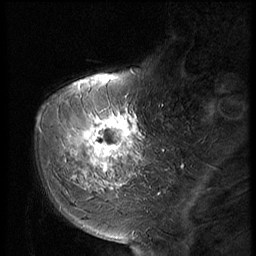
Breast MRI (dynamic contrast-enhanced), one sagittal slice. Position 16 of 56 along the scan axis. Dynamic contrast-enhanced series, image 2 of 2 at this slice position (ordered by acquisition). 1.5 T. TE 4.2 ms, TR 9 ms. 2.5 mm slice thickness. 256 × 256 image matrix, field of view 180 × 180 mm. Female patient, age 51 years. From the clinical record (not read from this slice): setting: breast cancer imaged before/during neoadjuvant chemotherapy; receptor status: triple-negative.
Outlined on this slice (semi-automatically segmented with operator editing):
- analysis volume of interest (the breast-tissue region the enhancement analysis was run in; not a lesion): box from (x=60, y=98) to (x=147, y=197) px
- tumour enhancement mask (voxels above the 140 % enhancement threshold inside the analysis volume of interest): (x=68, y=108)–(x=141, y=187)